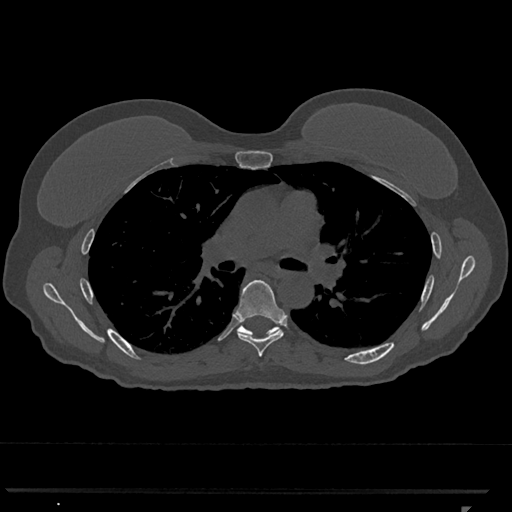
CT including the spine, one axial slice; slice 750 of 793 in the series (ordered by position); reconstruction kernel Br40s/3; bone window (W 1800 / L 400 HU); 0.5 mm slice thickness; 512 × 512 image matrix. Patient: female, 62 years. Case-level facts recorded for this patient, not image findings: primary cancer: renal.
Structures marked on this image (semi-automatic segmentation, software-assisted and operator-edited):
- T6 vertebra: bounding box (x1, y1, x2, y2) in pixels: (237, 279, 285, 357)
- T7 vertebra: (237, 323, 279, 336)